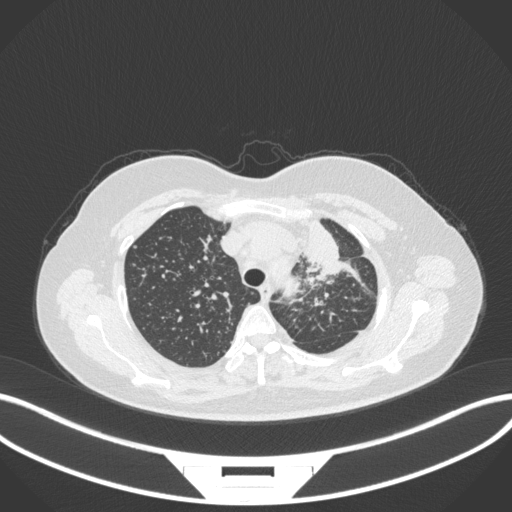
Chest CT, one axial slice. Slice 262 of 348 in the series (ordered by position). Reconstruction kernel B31f. 120 kVp. Lung window (W 1500 / L -600 HU). 512 × 512 image matrix, field of view 400 × 400 mm. Female patient, age 49 years. From the clinical record (not read from this slice): clinical TNM (as recorded): T1c N0 M1.
Structures marked on this image (rectangle marked by the reading radiologist):
- lung tumour (recorded histology: adenocarcinoma): bounding box [x1, y1, x2, y2] px = [297, 209, 345, 286]